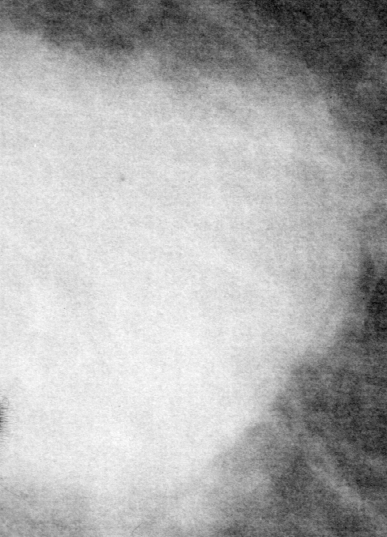
Region of interest cut from a scanned film mammogram (one marked finding), left breast, MLO view, BI-RADS breast density category 1 (scale 1–4).
- Mass, shape irregular, margins circumscribed / ill defined; BI-RADS assessment category 4; subtlety rating 5 on a 1 (subtle) to 5 (obvious) scale; pathology result (as recorded, not read from the image): malignant.